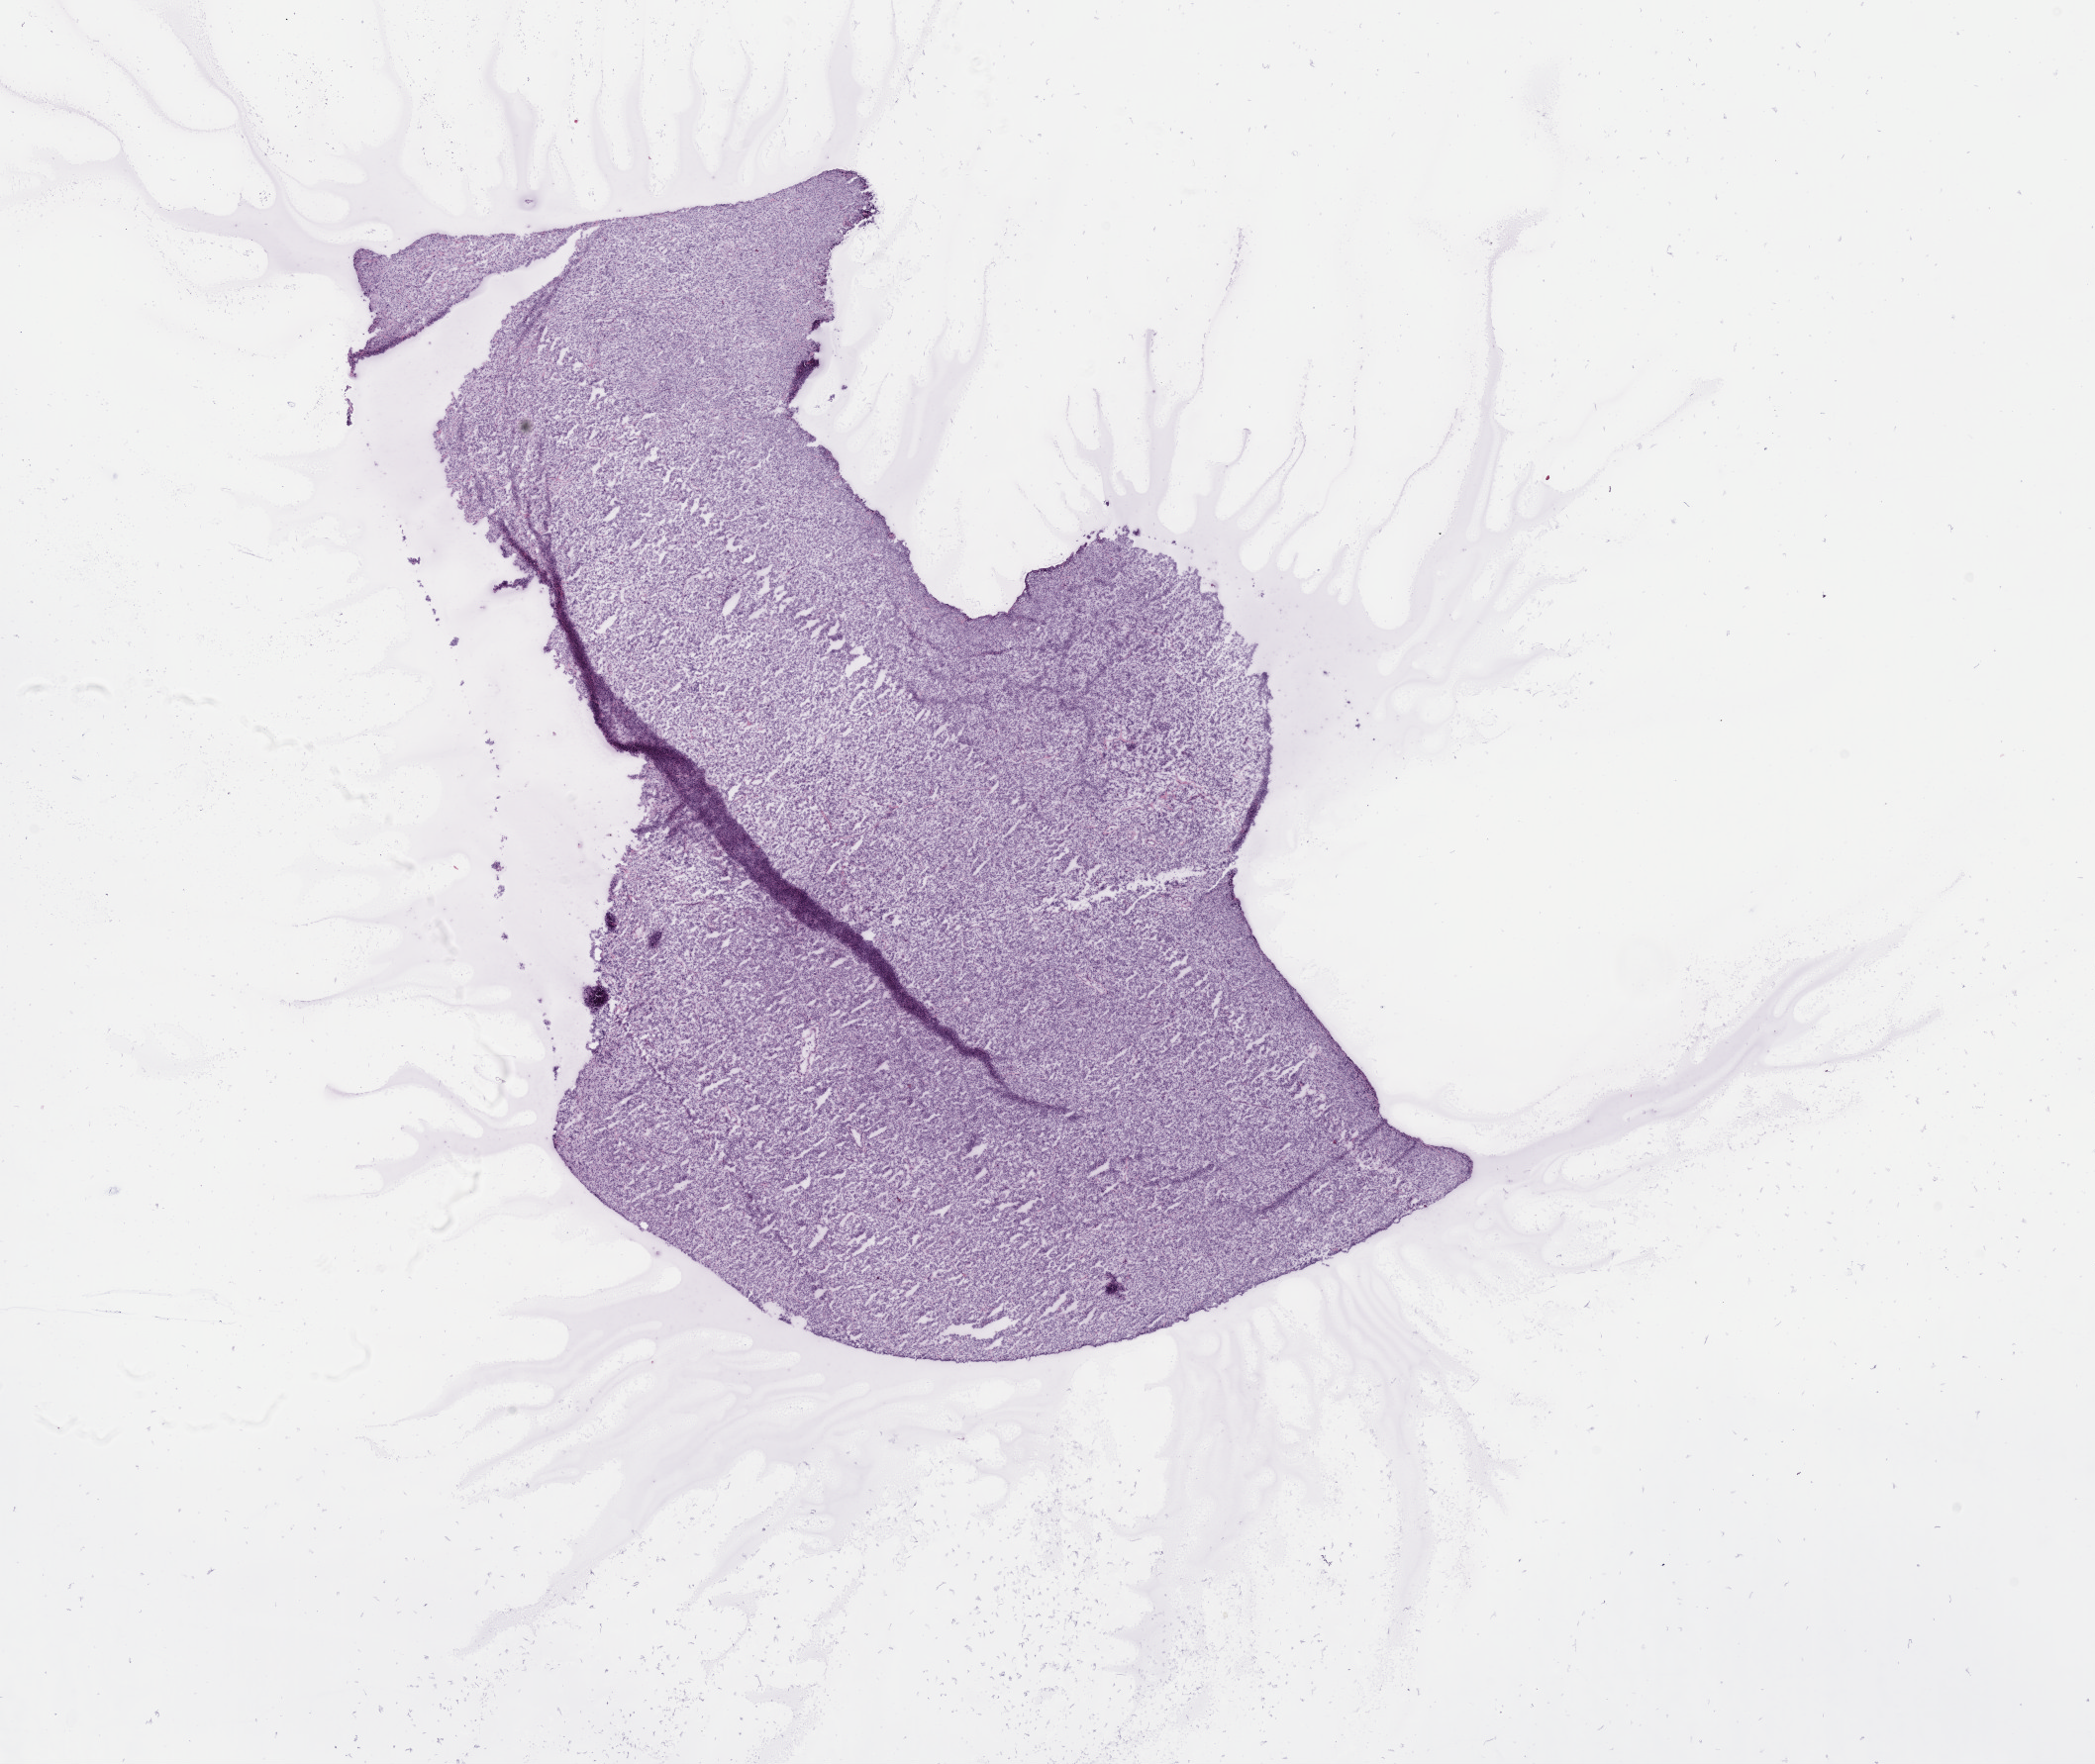
Whole-slide histology image, H&E, whole scanned area (about 17.1 x 14.4 mm) shown as a low-resolution overview, frozen section from the top of the tissue portion, primary tumour sample from the lymphoid tissue. Patient sex: female. Pathologist review of this section (percent, as recorded): tumour cells 90%, tumour nuclei 90%.
Pathologic diagnosis: Diffuse large B-cell lymphoma, NOS (lymph nodes of axilla or arm).